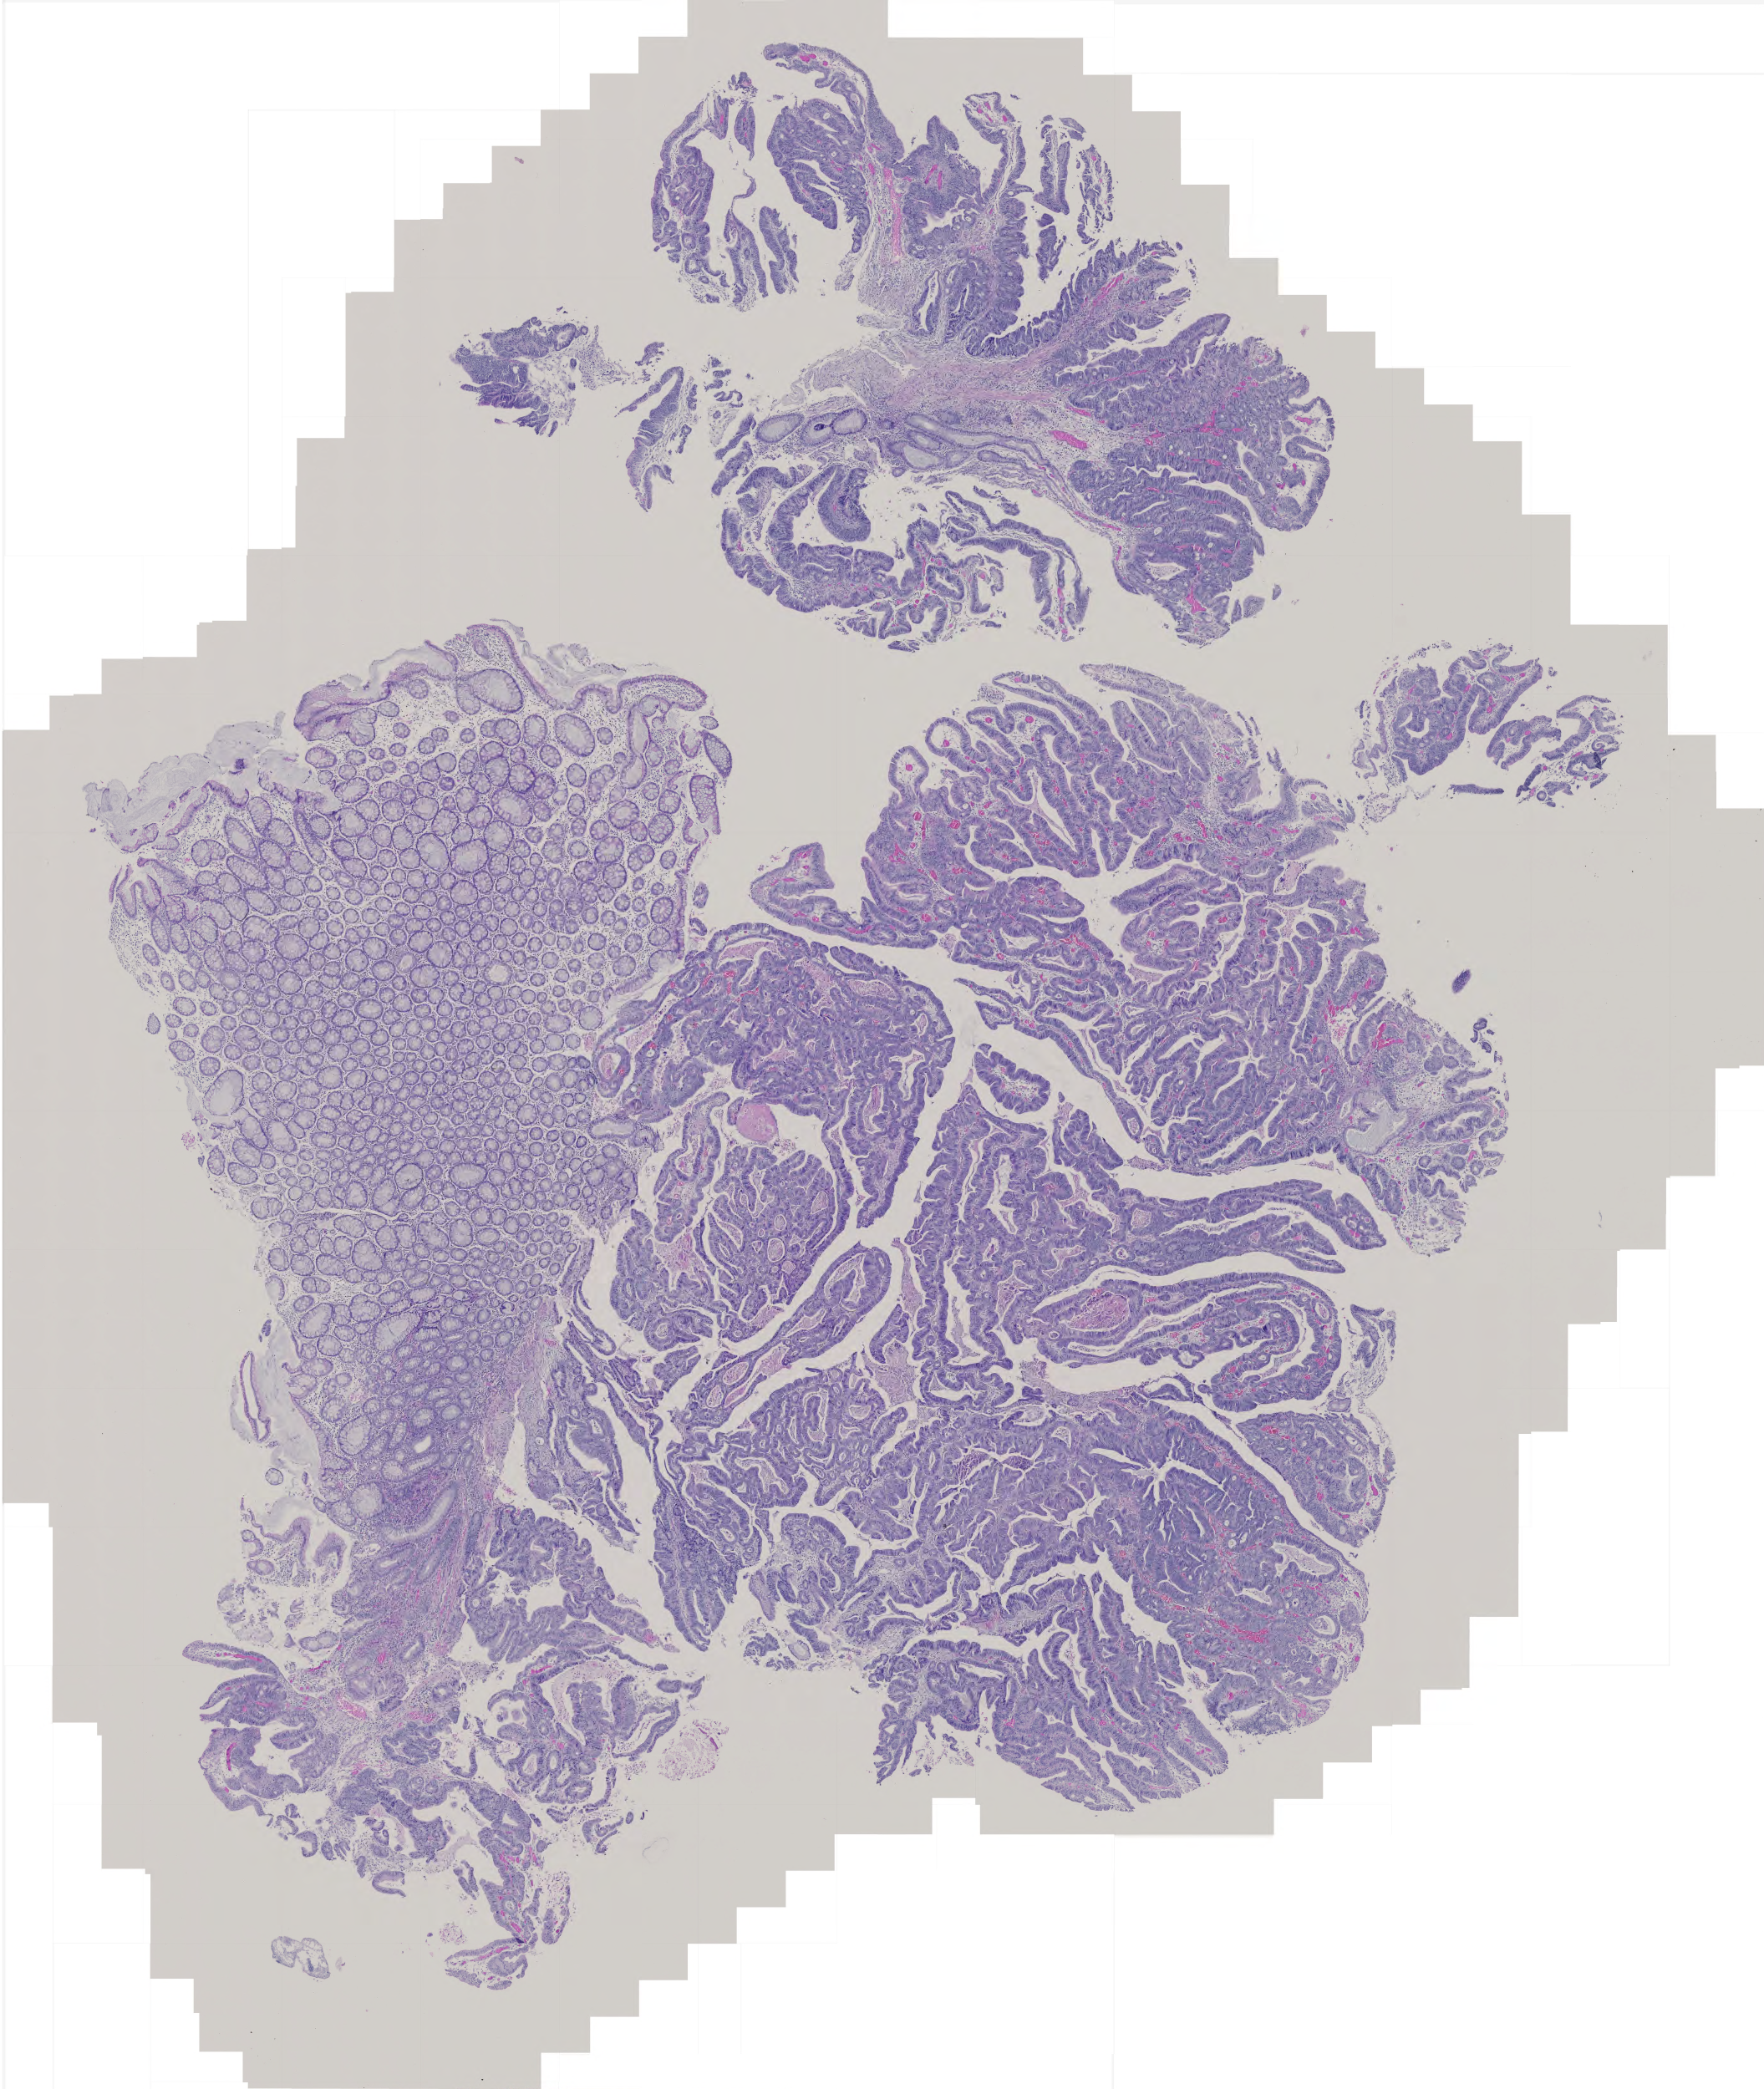
H&E-stained whole-slide image — a low-resolution overview of the entire scanned area, about 4.2 x 5.0 mm, formalin-fixed paraffin-embedded (FFPE) diagnostic section, primary tumour sample from the colon. Male, age 77 years at initial diagnosis.
Pathologic diagnosis: Adenocarcinoma, NOS.